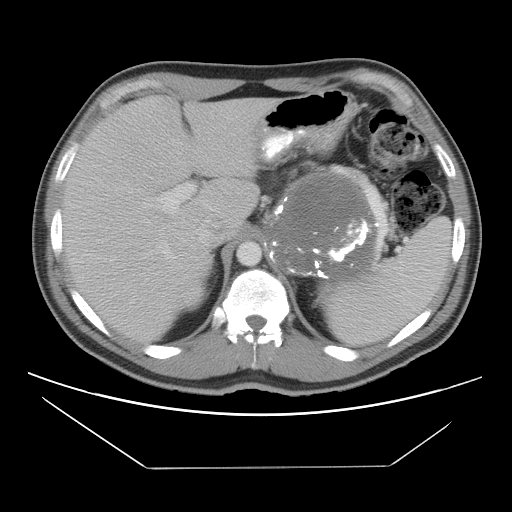
Contrast-enhanced abdominal CT, one axial slice; position 76 of 131 along the scan axis; intravenous contrast given; soft-tissue window (W 400 / L 40 HU); 5 mm slice thickness; 512 × 512 image matrix, field of view 396 × 396 mm. Patient: male, 44 years. Case-level facts recorded for this patient, not image findings: diagnosis: adrenocortical carcinoma; tumour side: left adrenal; tumour size at pathology: 15.5 cm; Ki-67 index: 6 %.
Structures marked on this image (semi-automatically segmented with operator editing):
- mass: bounding box (x1, y1, x2, y2) in pixels: (264, 173, 375, 278)